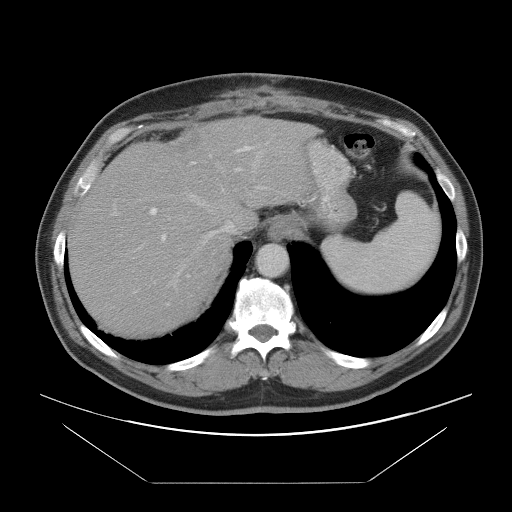
Contrast-enhanced abdominal CT, one axial slice; position 71 of 97 along the scan axis; 120 kVp; intravenous contrast given; soft-tissue window (W 400 / L 40 HU); 512 × 512 image matrix, field of view 442 × 442 mm. Male patient, age 62 years. Case-level facts recorded for this patient, not image findings: diagnosis: colorectal cancer liver metastases, imaged before liver resection; multiple liver metastases: no; largest metastasis: 7 cm; chemotherapy before resection: yes.
Annotated regions visible in this slice (expert manual segmentation):
- hepatic veins: bounding box (x1, y1, x2, y2) in pixels: (168, 139, 281, 287)
- liver: (70, 120, 309, 332)
- planned liver remnant (the part of the liver to remain after resection): (70, 170, 230, 332)
- portal vein (with intrahepatic branches): (113, 146, 264, 293)
- liver metastasis: (171, 134, 199, 153)